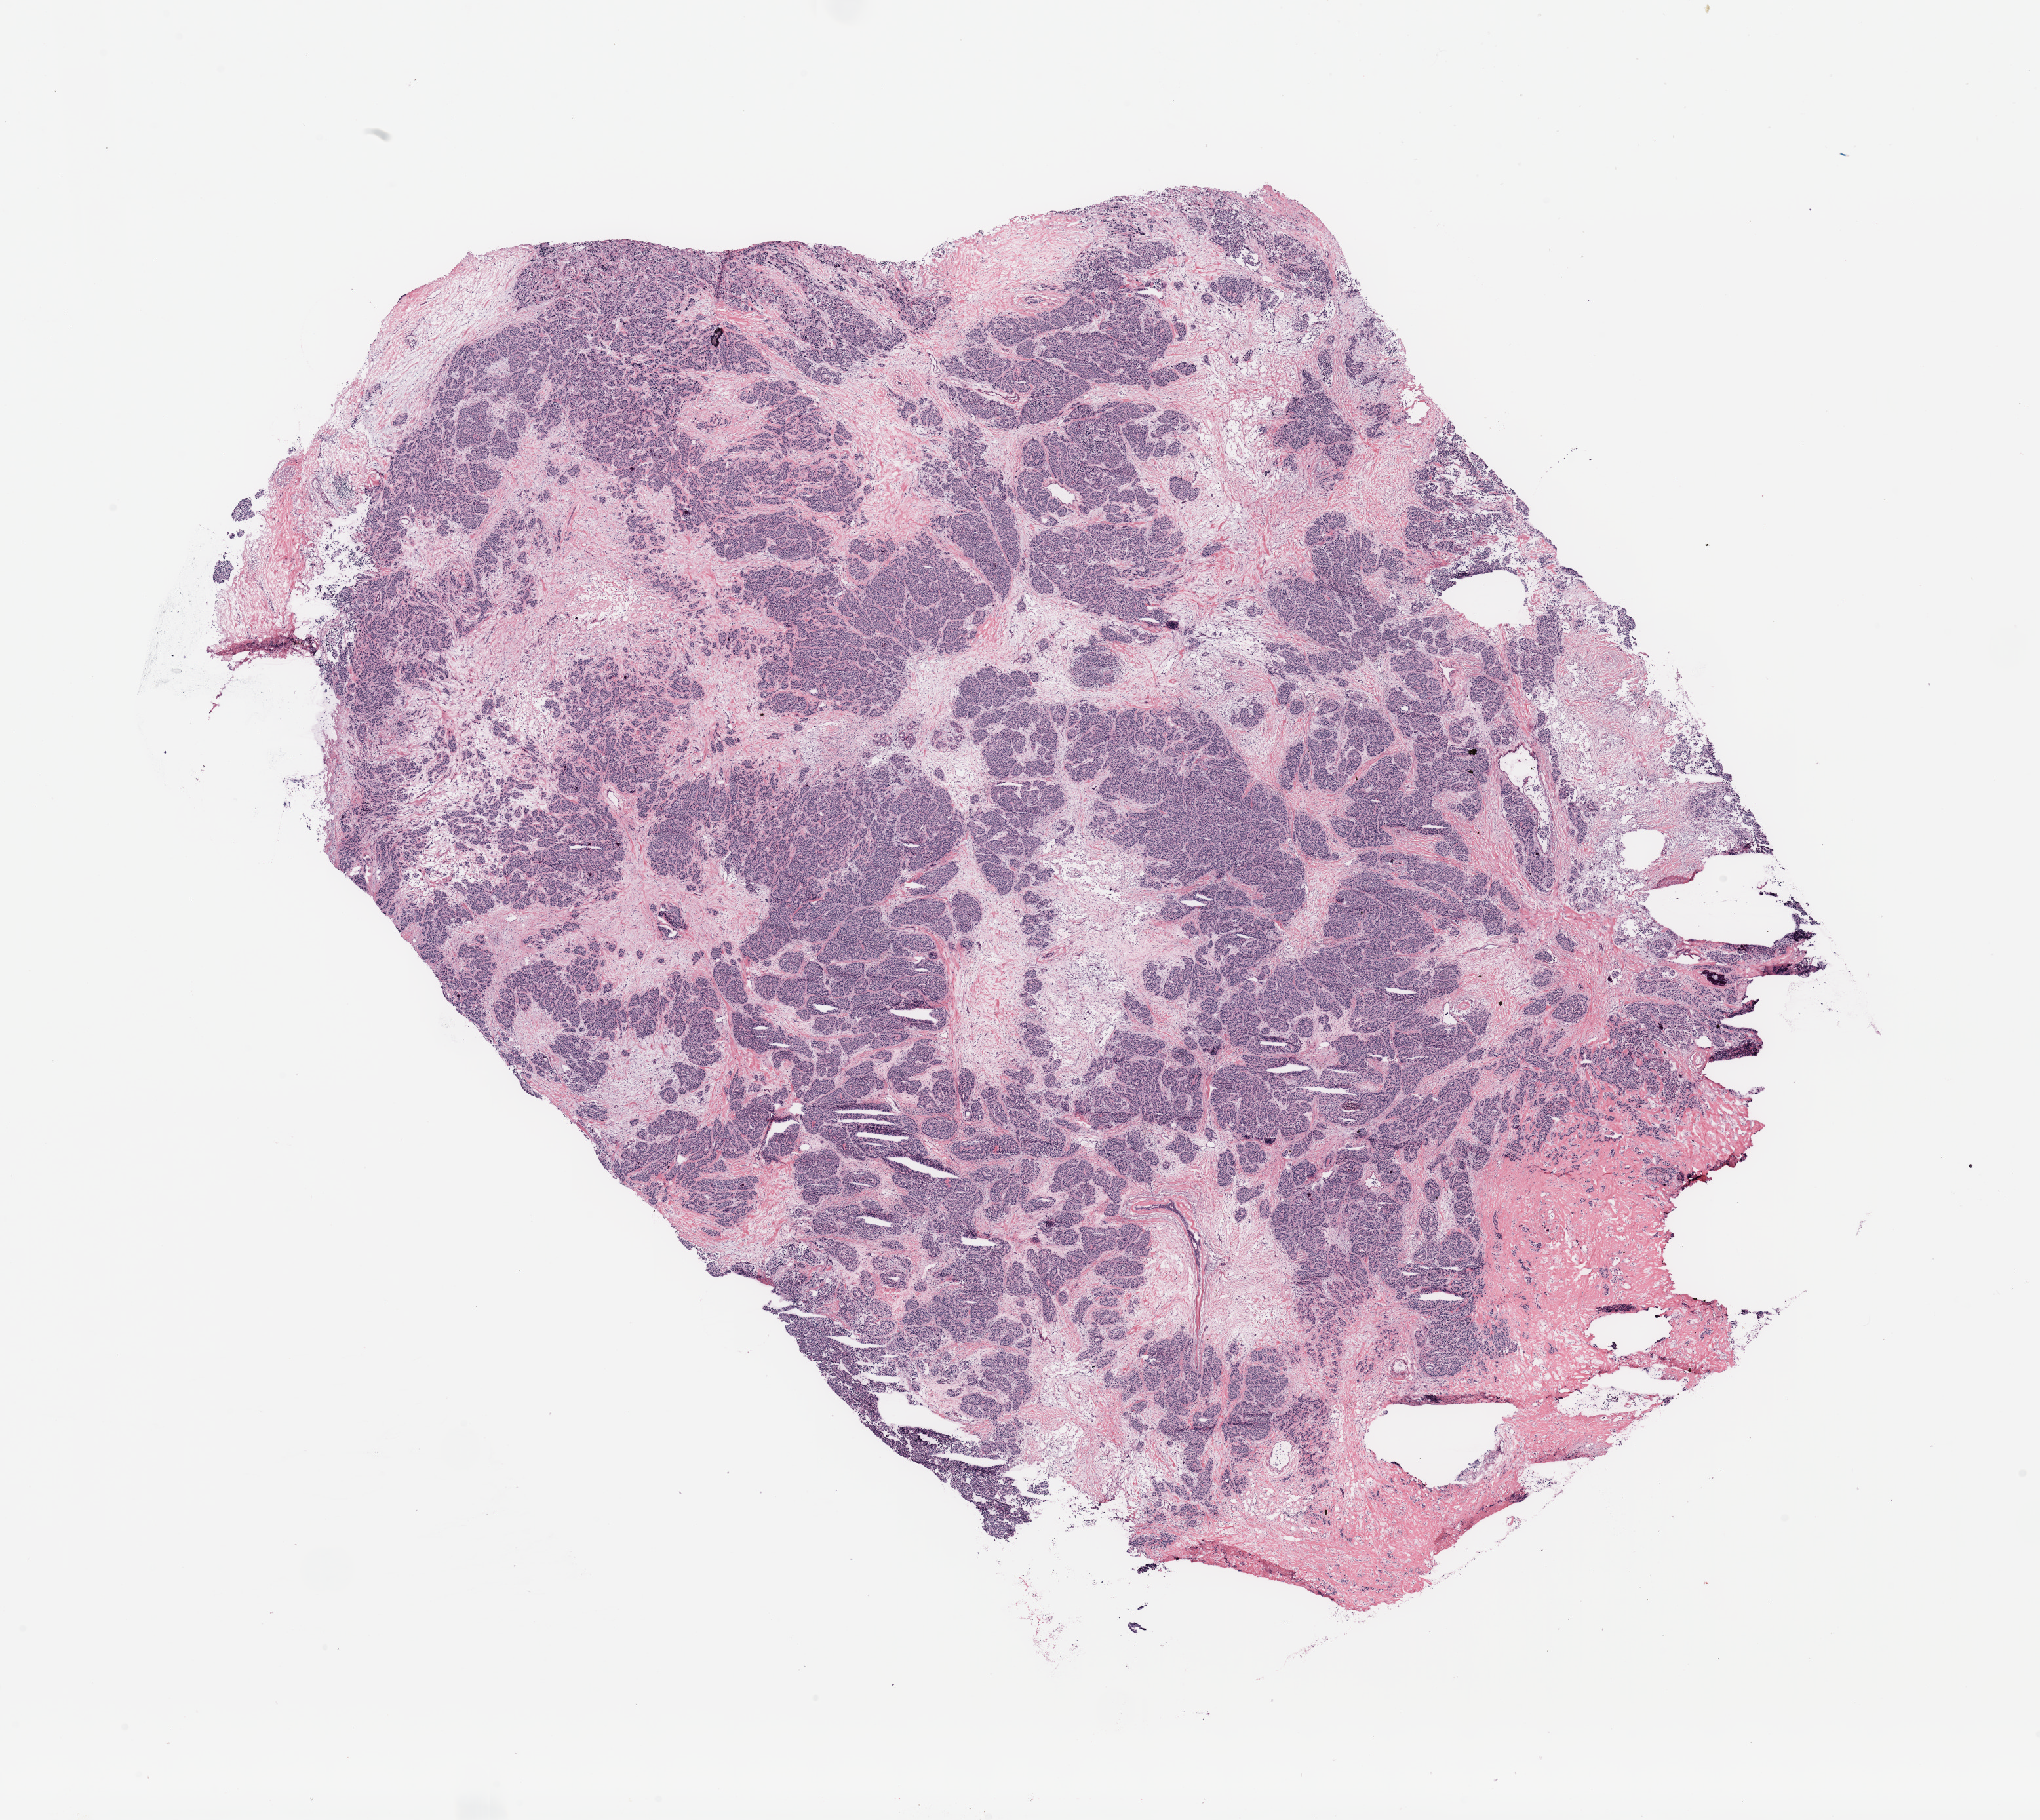
Hematoxylin and eosin (H&E) stained whole-slide image, whole scanned area (about 24.6 x 22.0 mm, slide scanned at 20x) shown as a low-resolution overview. Breast, tumour tissue. Female, 77 y/o.
Diagnosis: Infiltrating duct carcinoma, NOS. AJCC pathologic stage: IIA.